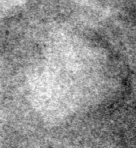
Cropped region of a digitized screen-film mammogram centred on a radiologist-marked abnormality, left breast, CC view.
Marked abnormality: mass, shape lymph node, margins circumscribed; BI-RADS assessment category 2; subtlety rating 4 on a 1 (subtle) to 5 (obvious) scale; benign without callback (not worked up further).